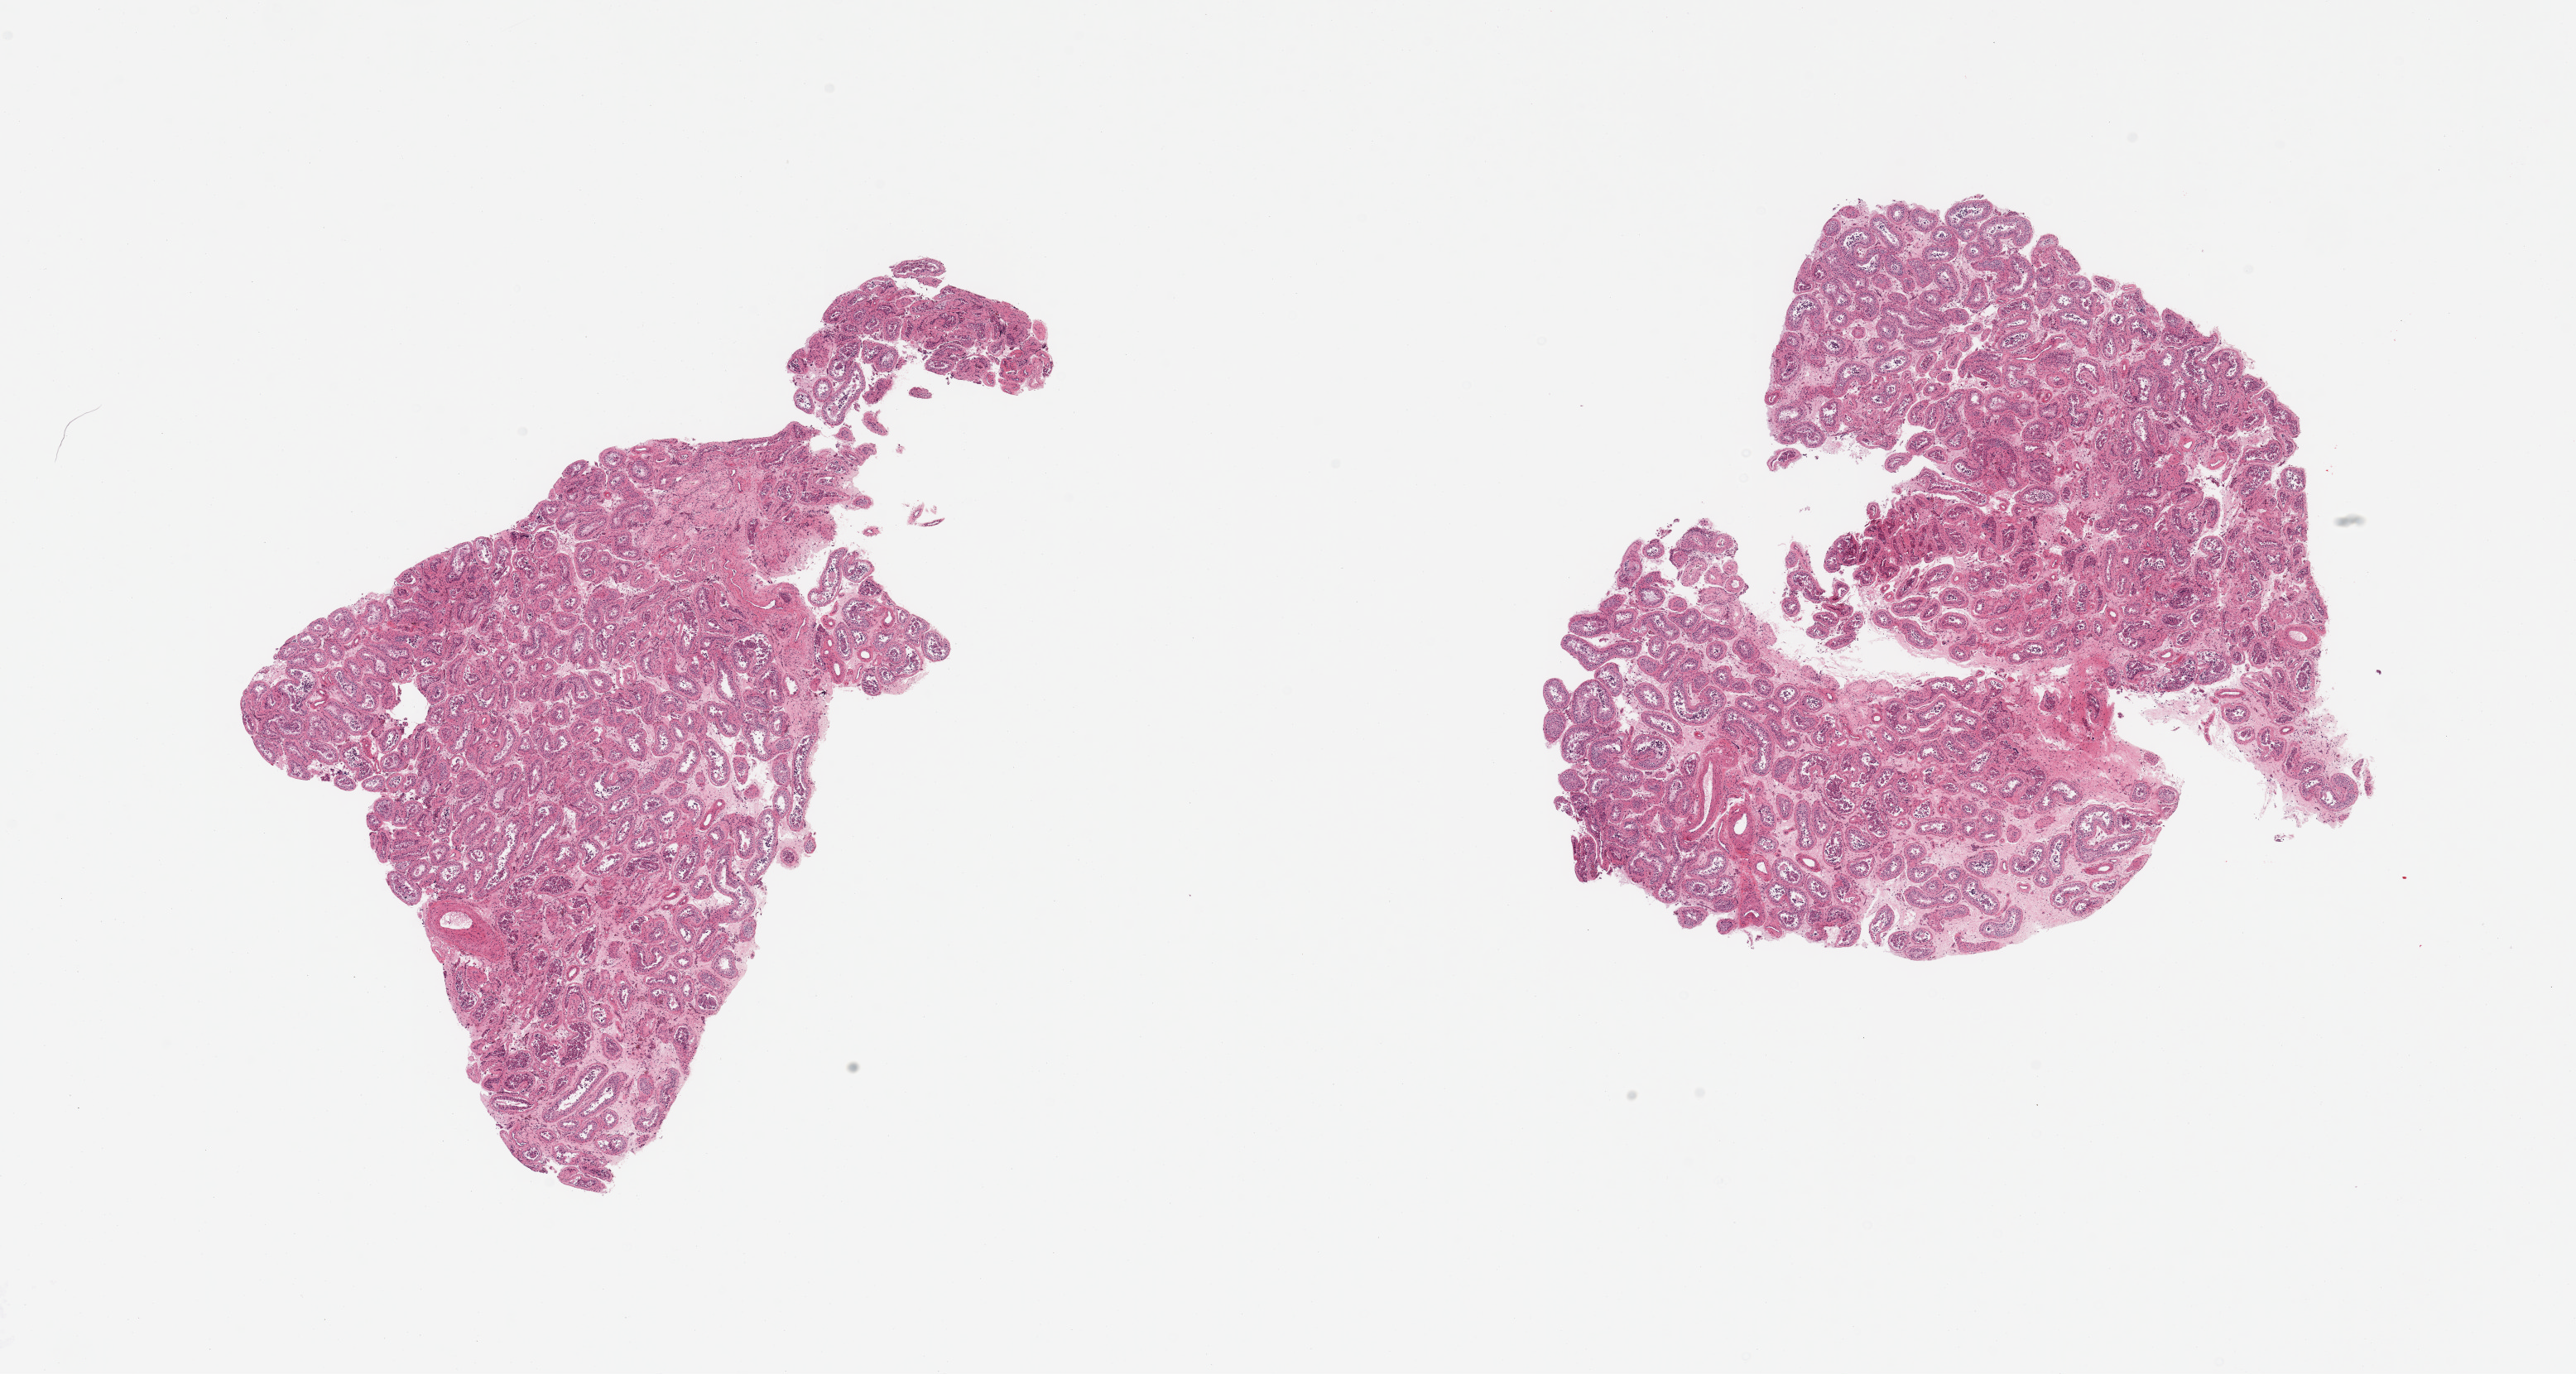
Whole-slide image, H&E stain — whole scanned area (about 24.6 x 13.1 mm, slide scanned at 20x) shown as a low-resolution overview, PAXgene-fixed, paraffin-embedded tissue, section of testis (target tissue), donor tissue sample. Donor: male.
Pathologist's review note for this sample: 2 pieces; greatly reduced mature spermatogenesis.